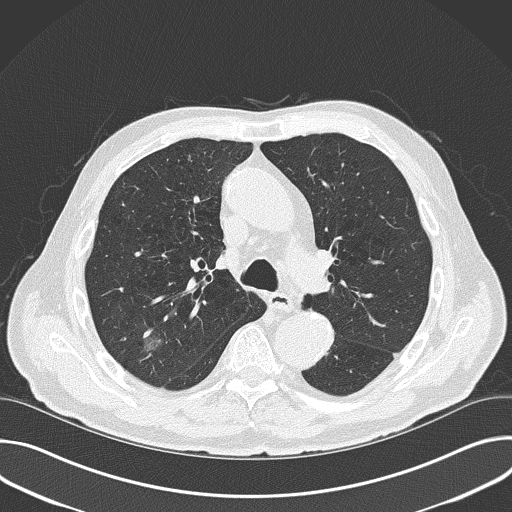
Chest CT (low-dose screening protocol), one axial image. Baseline annual screen. Lung window (W 1500 / L -600 HU). Lung (sharp) reconstruction kernel (B50f). Slice 109 of 177 in the series. Male participant, aged 74 years at enrolment. Former smoker at enrolment.
Expert reader's lesion annotation, box from (x=125, y=319) to (x=176, y=368) px. The screening reader recorded 3 non-calcified nodules or masses ≥4 mm on this exam; which of them this box marks is not recorded. Official screen result: positive, change unspecified: nodule(s) >= 4 mm or enlarging nodule(s), mass(es), or other non-specific abnormalities suspicious for lung cancer.